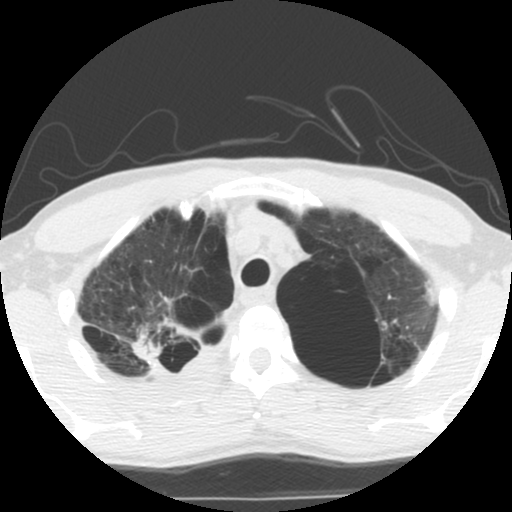
Chest CT (low-dose screening protocol), one axial image, second screening round (one year after baseline), lung window (W 1500 / L -600 HU), 2.5 mm slice thickness, standard (soft-tissue) reconstruction kernel (STANDARD), slice 95 of 119 in the series. Male participant, aged 62 years at enrolment. Current smoker at enrolment.
Expert reader's lesion annotation, bounding box (x1, y1, x2, y2) in pixels: (120, 317, 207, 387). Screening reader's record for this exam (one nodule recorded; not confirmed to be the boxed lesion): non-calcified nodule or mass ≥4 mm, 35 × 25 mm, soft tissue attenuation. Later outcome: lung cancer diagnosed 14 days after this screen — non-small cell carcinoma, right upper lobe, poorly differentiated (G3), stage IA (AJCC 6th edition), 70 mm at pathology.